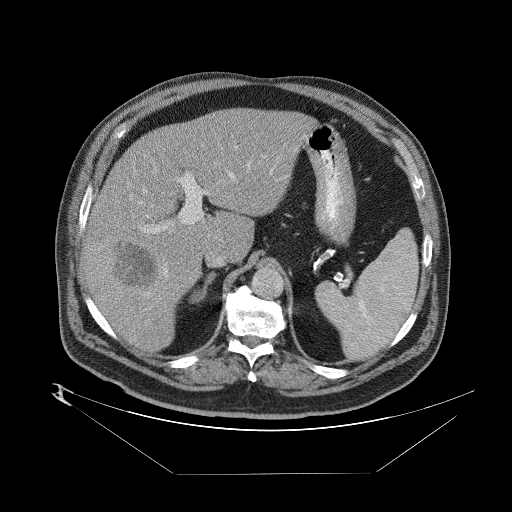
Contrast-enhanced abdominal CT (liver protocol), one axial slice; one of 2 acquisitions stored at this slice position; soft-tissue window (W 400 / L 40 HU); 2.5 mm slice thickness; 512 × 512 image matrix, field of view 480 × 480 mm. Case-level facts recorded for this patient, not image findings: diagnosis: hepatocellular carcinoma (patient treated with transarterial chemoembolisation; whether this scan precedes or follows treatment is not stated here); TNM stage (as recorded): Stage-II; Child-Pugh class: B.
Outlined on this slice (semi-automatic segmentation, software-assisted and operator-edited):
- abdominal aorta: bounding box <253,266,284,298> (left, top, right, bottom; pixels)
- liver parenchyma outside the tumour (the mass and vessels are separate outlines, so this box may not span the whole liver): <82,106,310,352>
- mass: <107,242,158,288>
- liver vessels: <86,161,222,336>